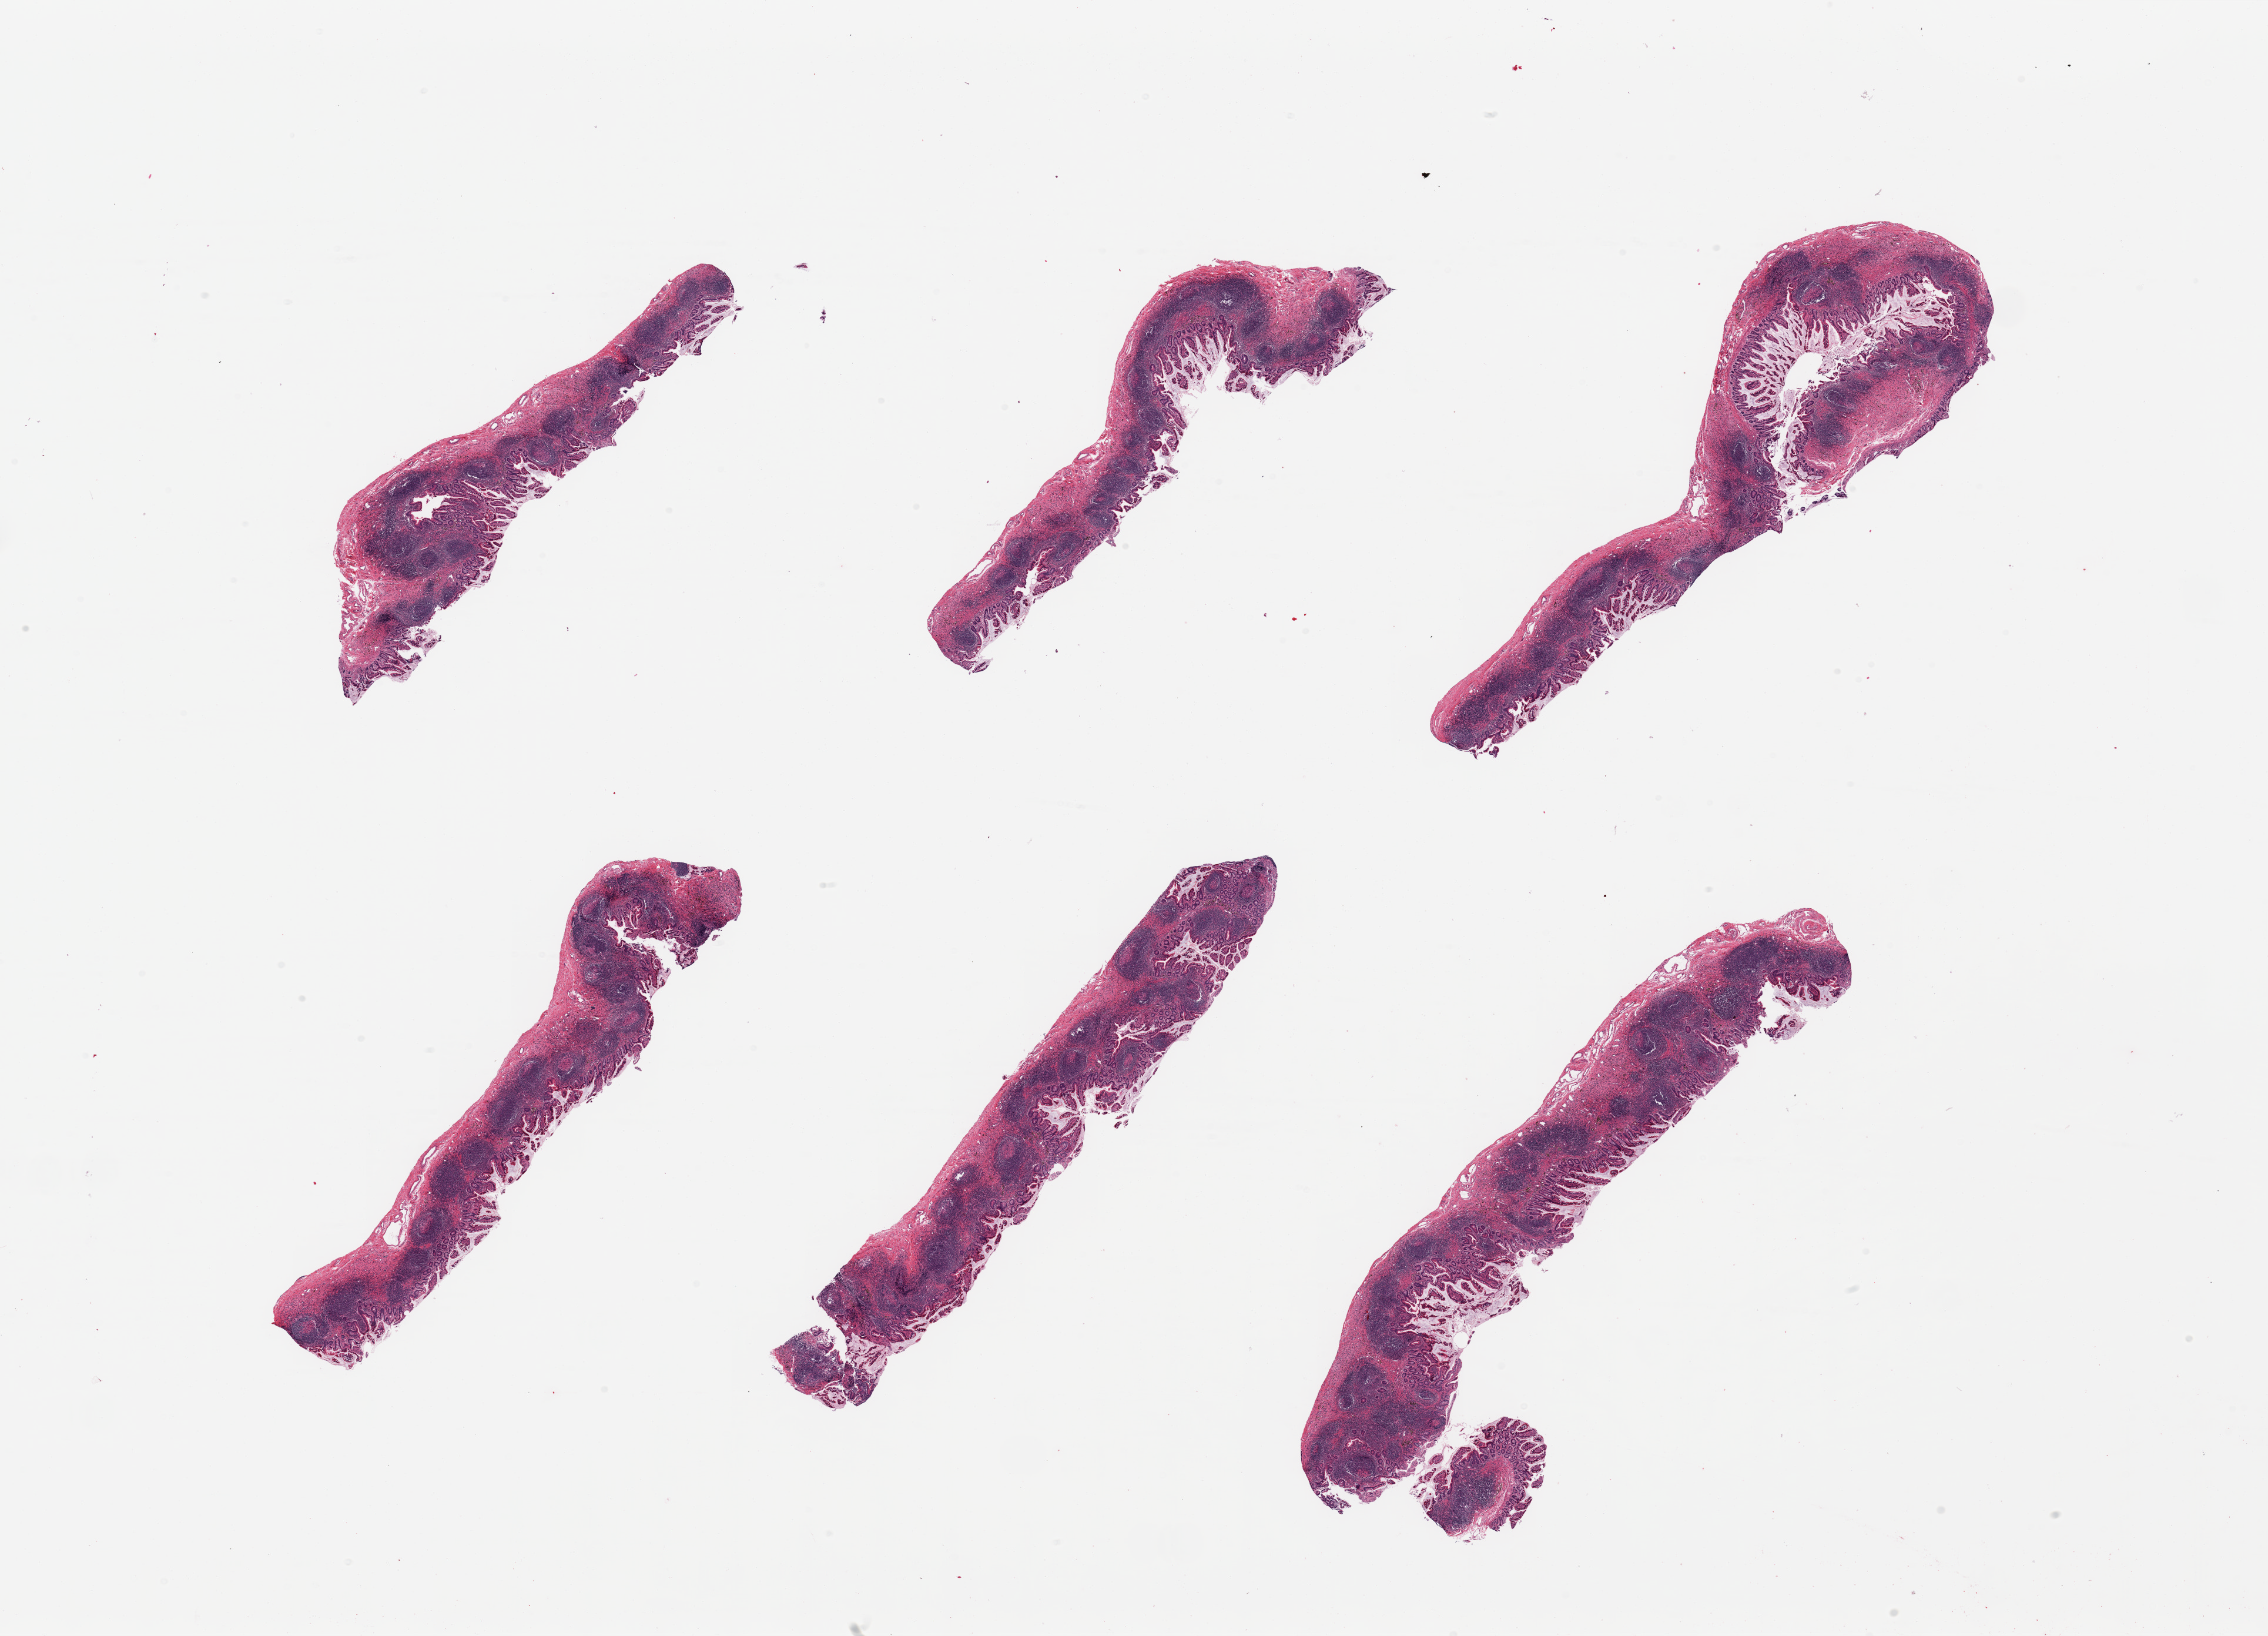
Whole-slide image, hematoxylin and eosin (H&E) stain, brightfield, a low-resolution overview of the entire scanned area, about 30.5 x 22.0 mm (from a 20x scan), PAXgene-fixed, paraffin-embedded tissue, section of ileum (target tissue), donor tissue sample. Donor sex: female.
Review note (as recorded): 6 pieces; preserved with excellent lymphoid component, pigmentation and reactive follicles.